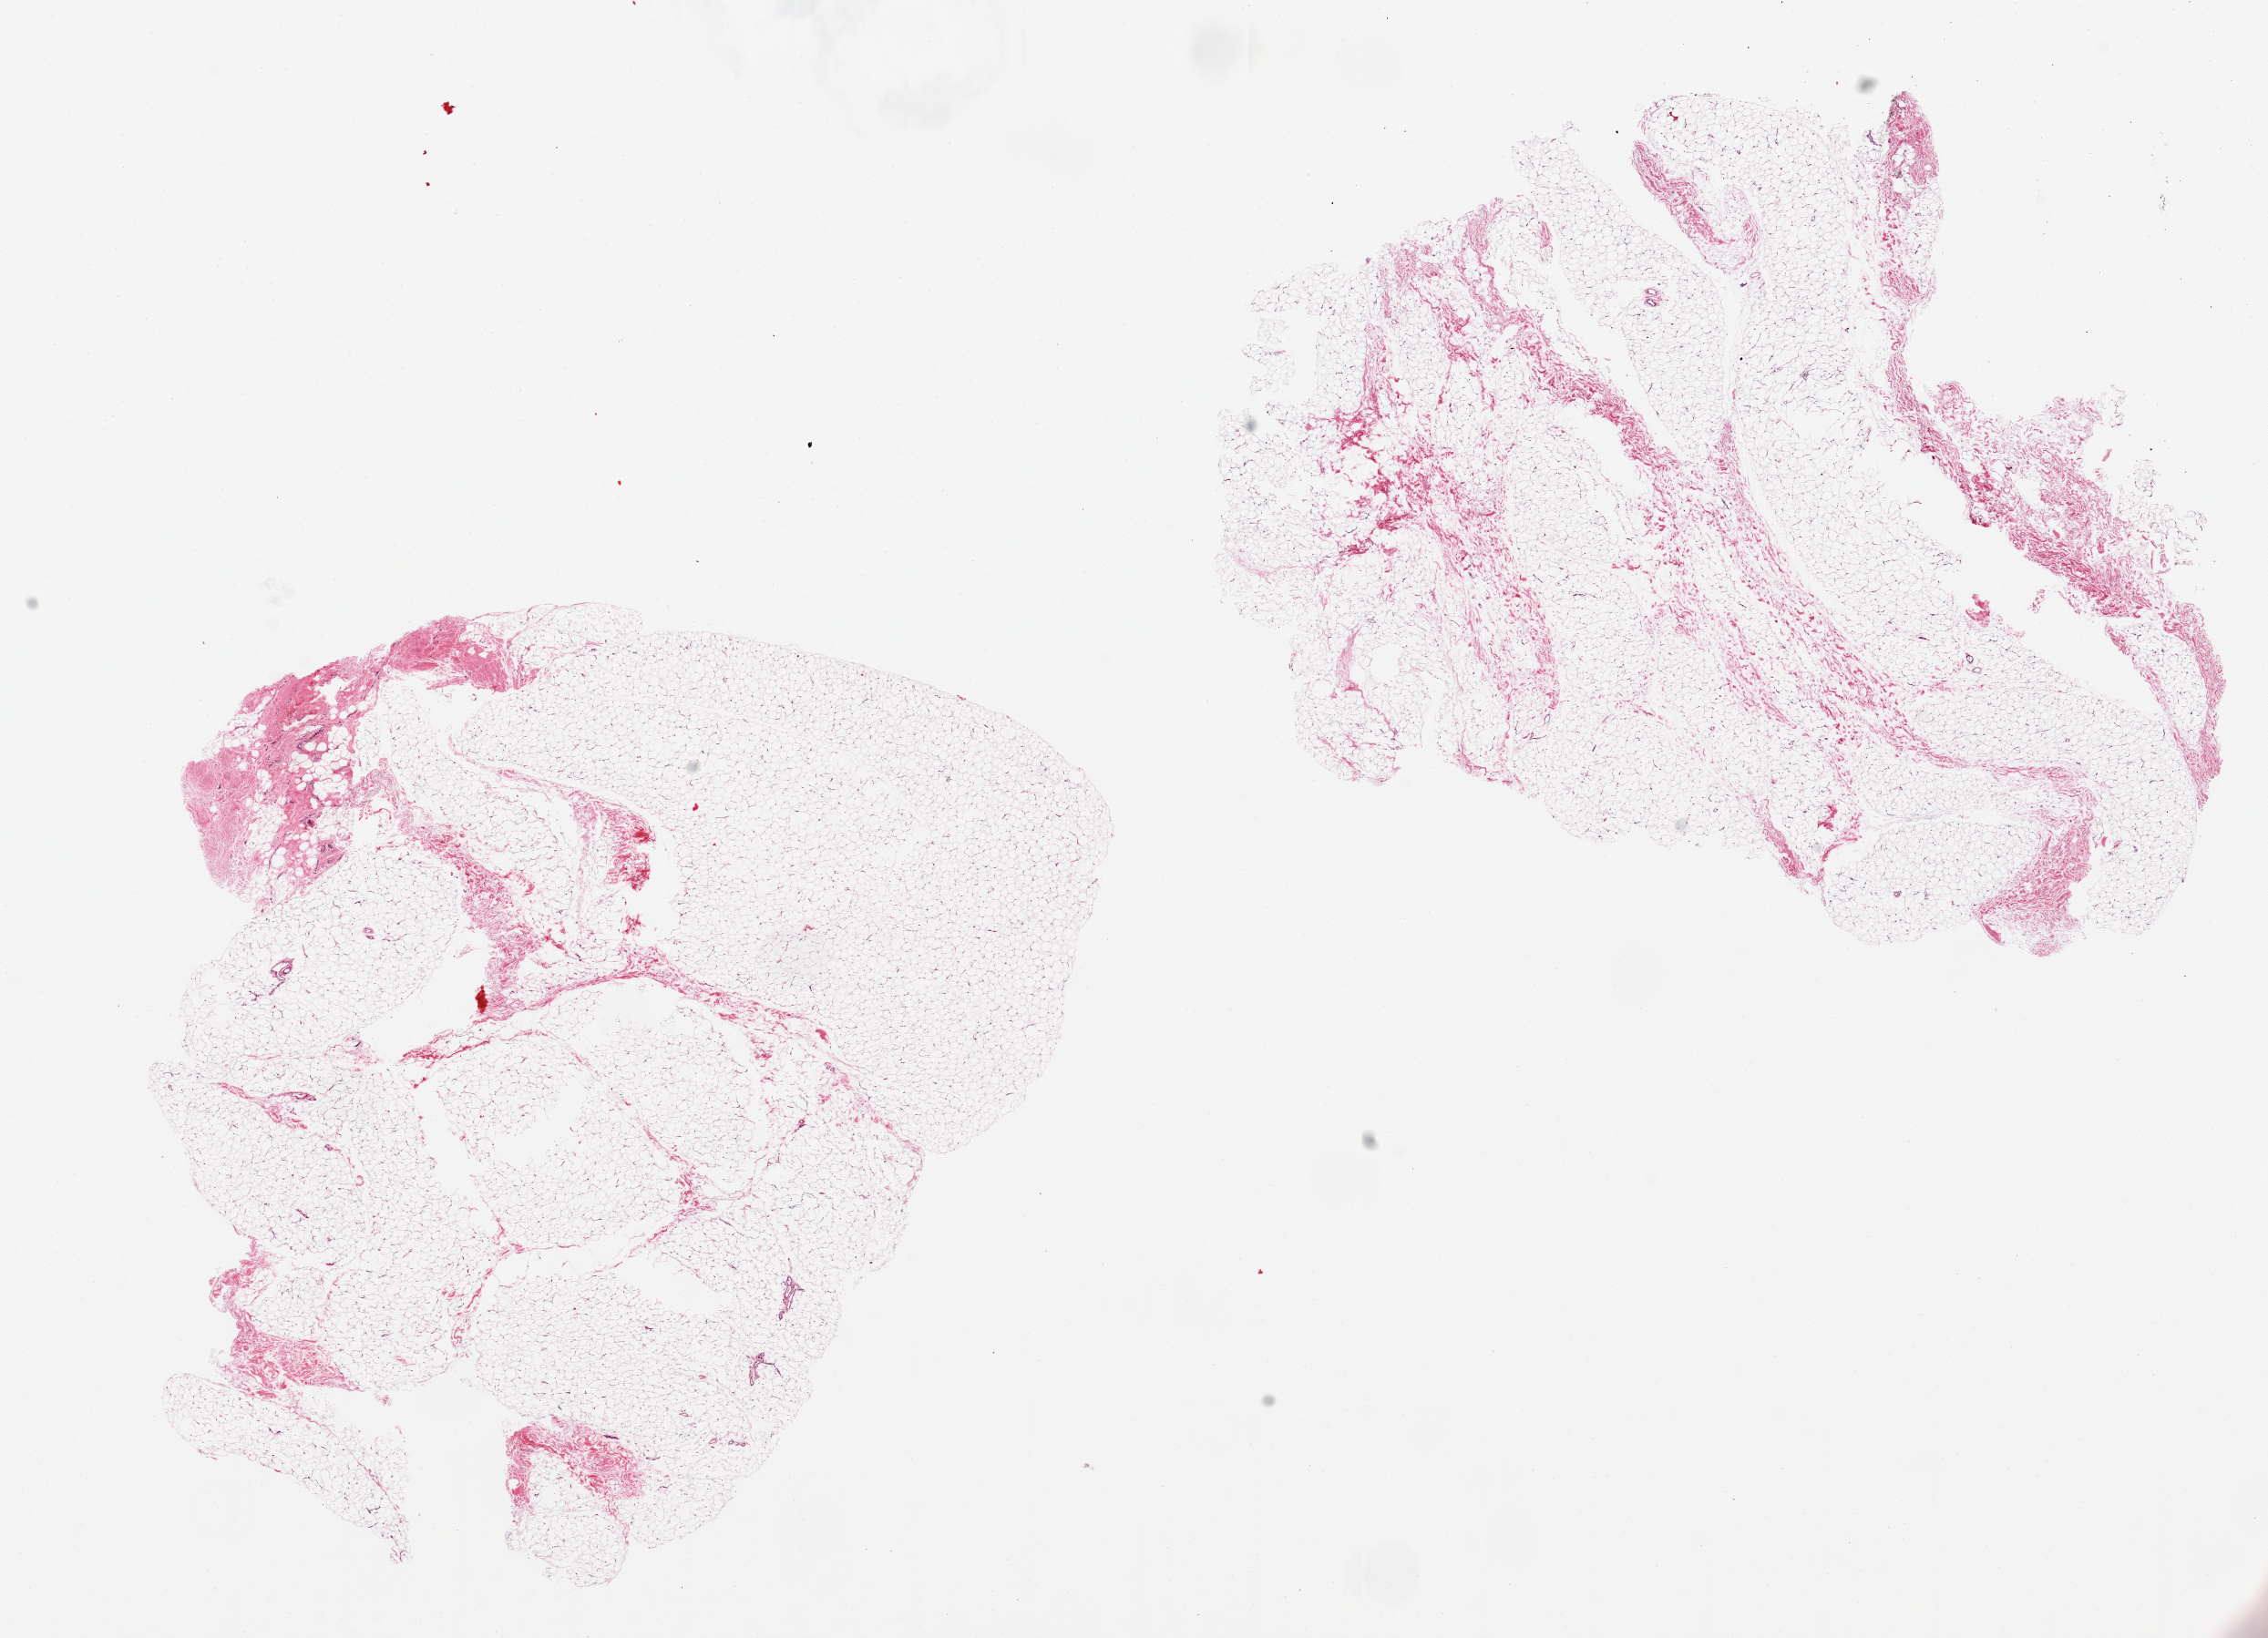
Whole-slide image, H&E stain, low-resolution overview of the scanned area, about 19.7 x 14.2 mm (slide scanned at 20x). PAXgene-fixed, paraffin-embedded tissue. Sampled site (target tissue): breast. Donor tissue sample. Male donor.
Review note (as recorded): 2 pieces, 8x8 & 8x7 mm; all adipose tissue; no mammary ducts.